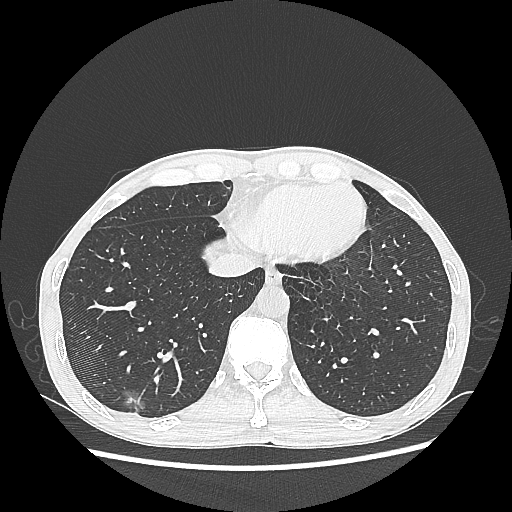
Chest CT, one axial slice; position 73 of 270 along the scan axis; reconstruction kernel LUNG; 100 kVp; lung window (W 1500 / L -600 HU); 1.25 mm slice thickness; 512 × 512 image matrix, field of view 360 × 360 mm. Patient: male, 60 years. From the clinical record (not read from this slice): clinical TNM (as recorded): T1c N0 M0; histopathological grade: G2.
Structures marked on this image (rectangle marked by the reading radiologist):
- lung tumour (recorded histology: adenocarcinoma): bounding box [x1, y1, x2, y2] px = [115, 382, 148, 418]